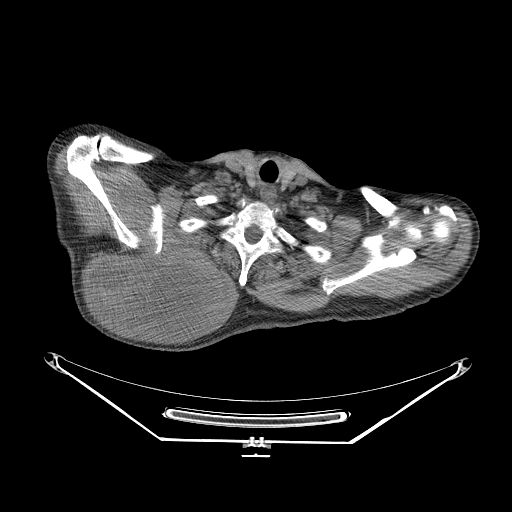
CT of an extremity soft-tissue mass (from a PET/CT study), one axial slice. Position 207 of 267 along the scan axis. Reconstruction kernel STANDARD. Soft-tissue window (W 400 / L 40 HU). 3.75 mm slice thickness. 512 × 512 image matrix, field of view 500 × 500 mm. Male patient. From the clinical record (not read from this slice): histological type: pleiomorphic spindle cell undifferentiated; grade: high; site of the primary tumour: right parascapusular.
Outlined on this slice (expert contour drawn on MRI and transferred to this co-registered scan by the dataset authors):
- gross tumour volume including surrounding oedema: bounding box <87,237,232,328> (left, top, right, bottom; pixels)
- gross tumour volume (mass): <89,240,225,325>